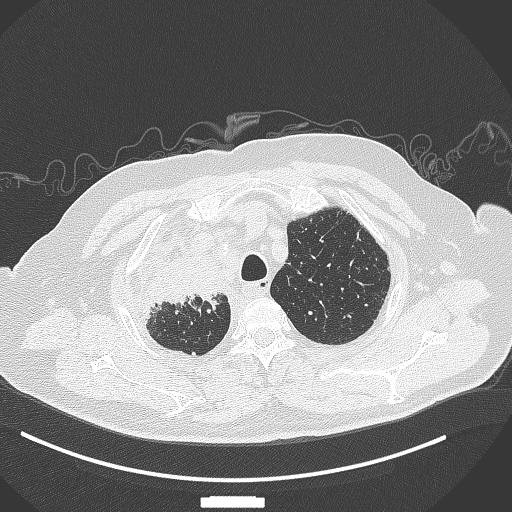
Chest CT, one axial slice; slice 308 of 384 in the series (ordered by position); lung window (W 1500 / L -600 HU); 1 mm slice thickness; 512 × 512 image matrix. Patient: male, 69 years. Case-level facts recorded for this patient, not image findings: clinical TNM (as recorded): T4 N3 M1.
Outlined on this slice (bounding box drawn by a radiologist):
- lung tumour (recorded histology: adenocarcinoma): bounding box <140,248,221,319> (left, top, right, bottom; pixels)